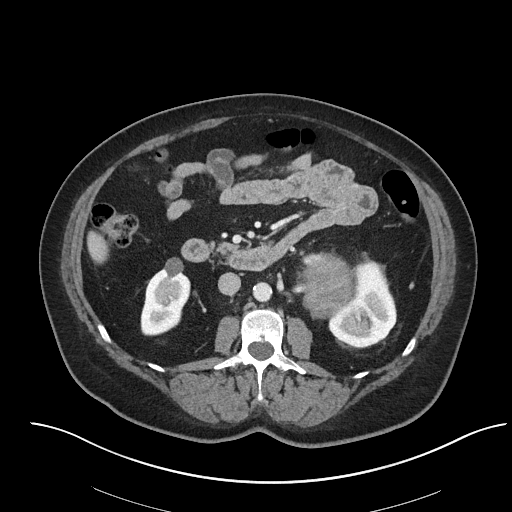
Contrast-enhanced abdominal CT, one axial slice; position 30 of 92 along the scan axis; soft-tissue window (W 400 / L 40 HU); 512 × 512 image matrix. Patient: female, 53 years. From the clinical record (not read from this slice): diagnosis: adrenocortical carcinoma; tumour side: left adrenal; tumour size at pathology: 9 cm; Ki-67 index: 28 %; stage (as recorded): 2.
Annotated regions visible in this slice (semi-automatically segmented with operator editing):
- mass: bounding box <306,253,352,317> (left, top, right, bottom; pixels)